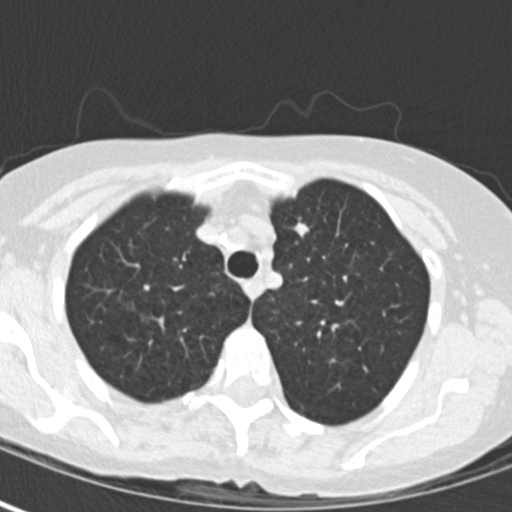
Low-dose screening chest CT, one axial slice. Position 125 of 163 along the scan axis. Reconstruction kernel B30f. Lung window (W 1500 / L -600 HU). 2 mm slice thickness. 512 × 512 image matrix.
Structures marked on this image (manually delineated by an expert):
- lesion 1 (tumor, upper lobe of left lung): bounding box <294,218,309,237> (left, top, right, bottom; pixels)